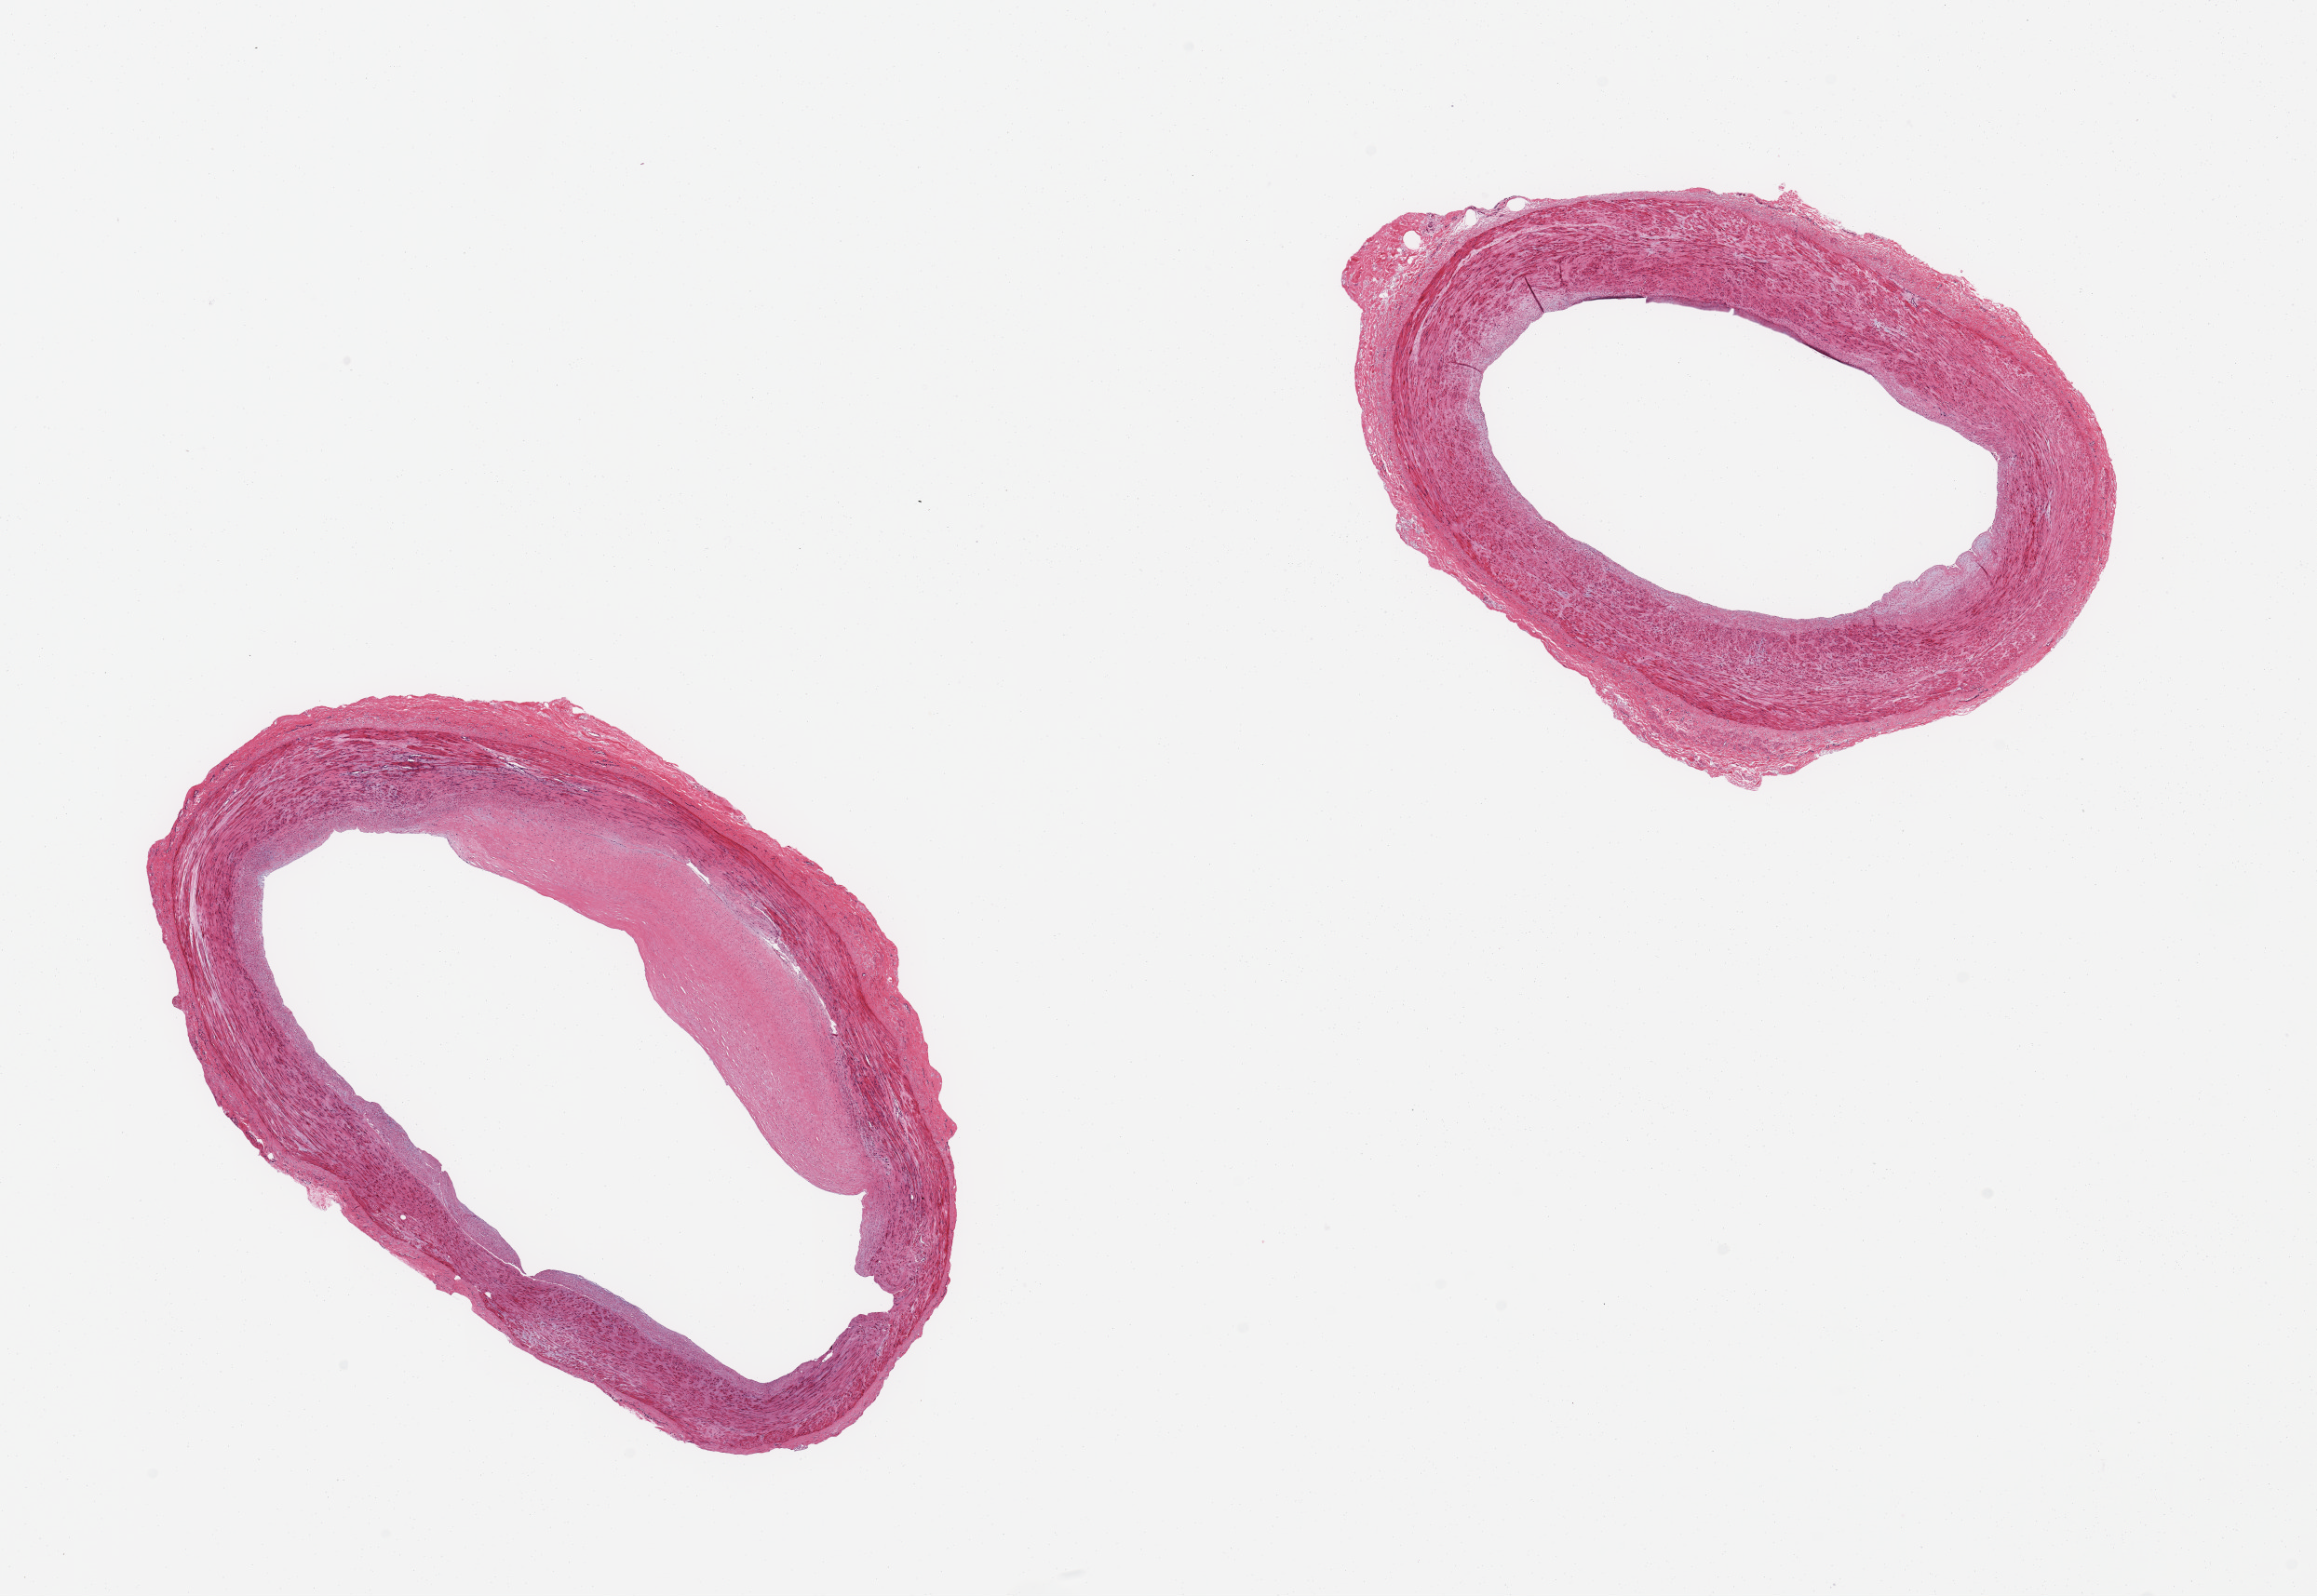
Digitized hematoxylin and eosin (H&E)-stained section — a low-resolution overview of the entire scanned area, about 19.7 x 13.6 mm (slide scanned at 20x); PAXgene-fixed, paraffin-embedded tissue; section of tibial artery (target tissue); tissue donor sample.
• review note (as recorded): 2 pieces; well trimmed vessels 1 with eccentric fibrous plaque 1mm thick